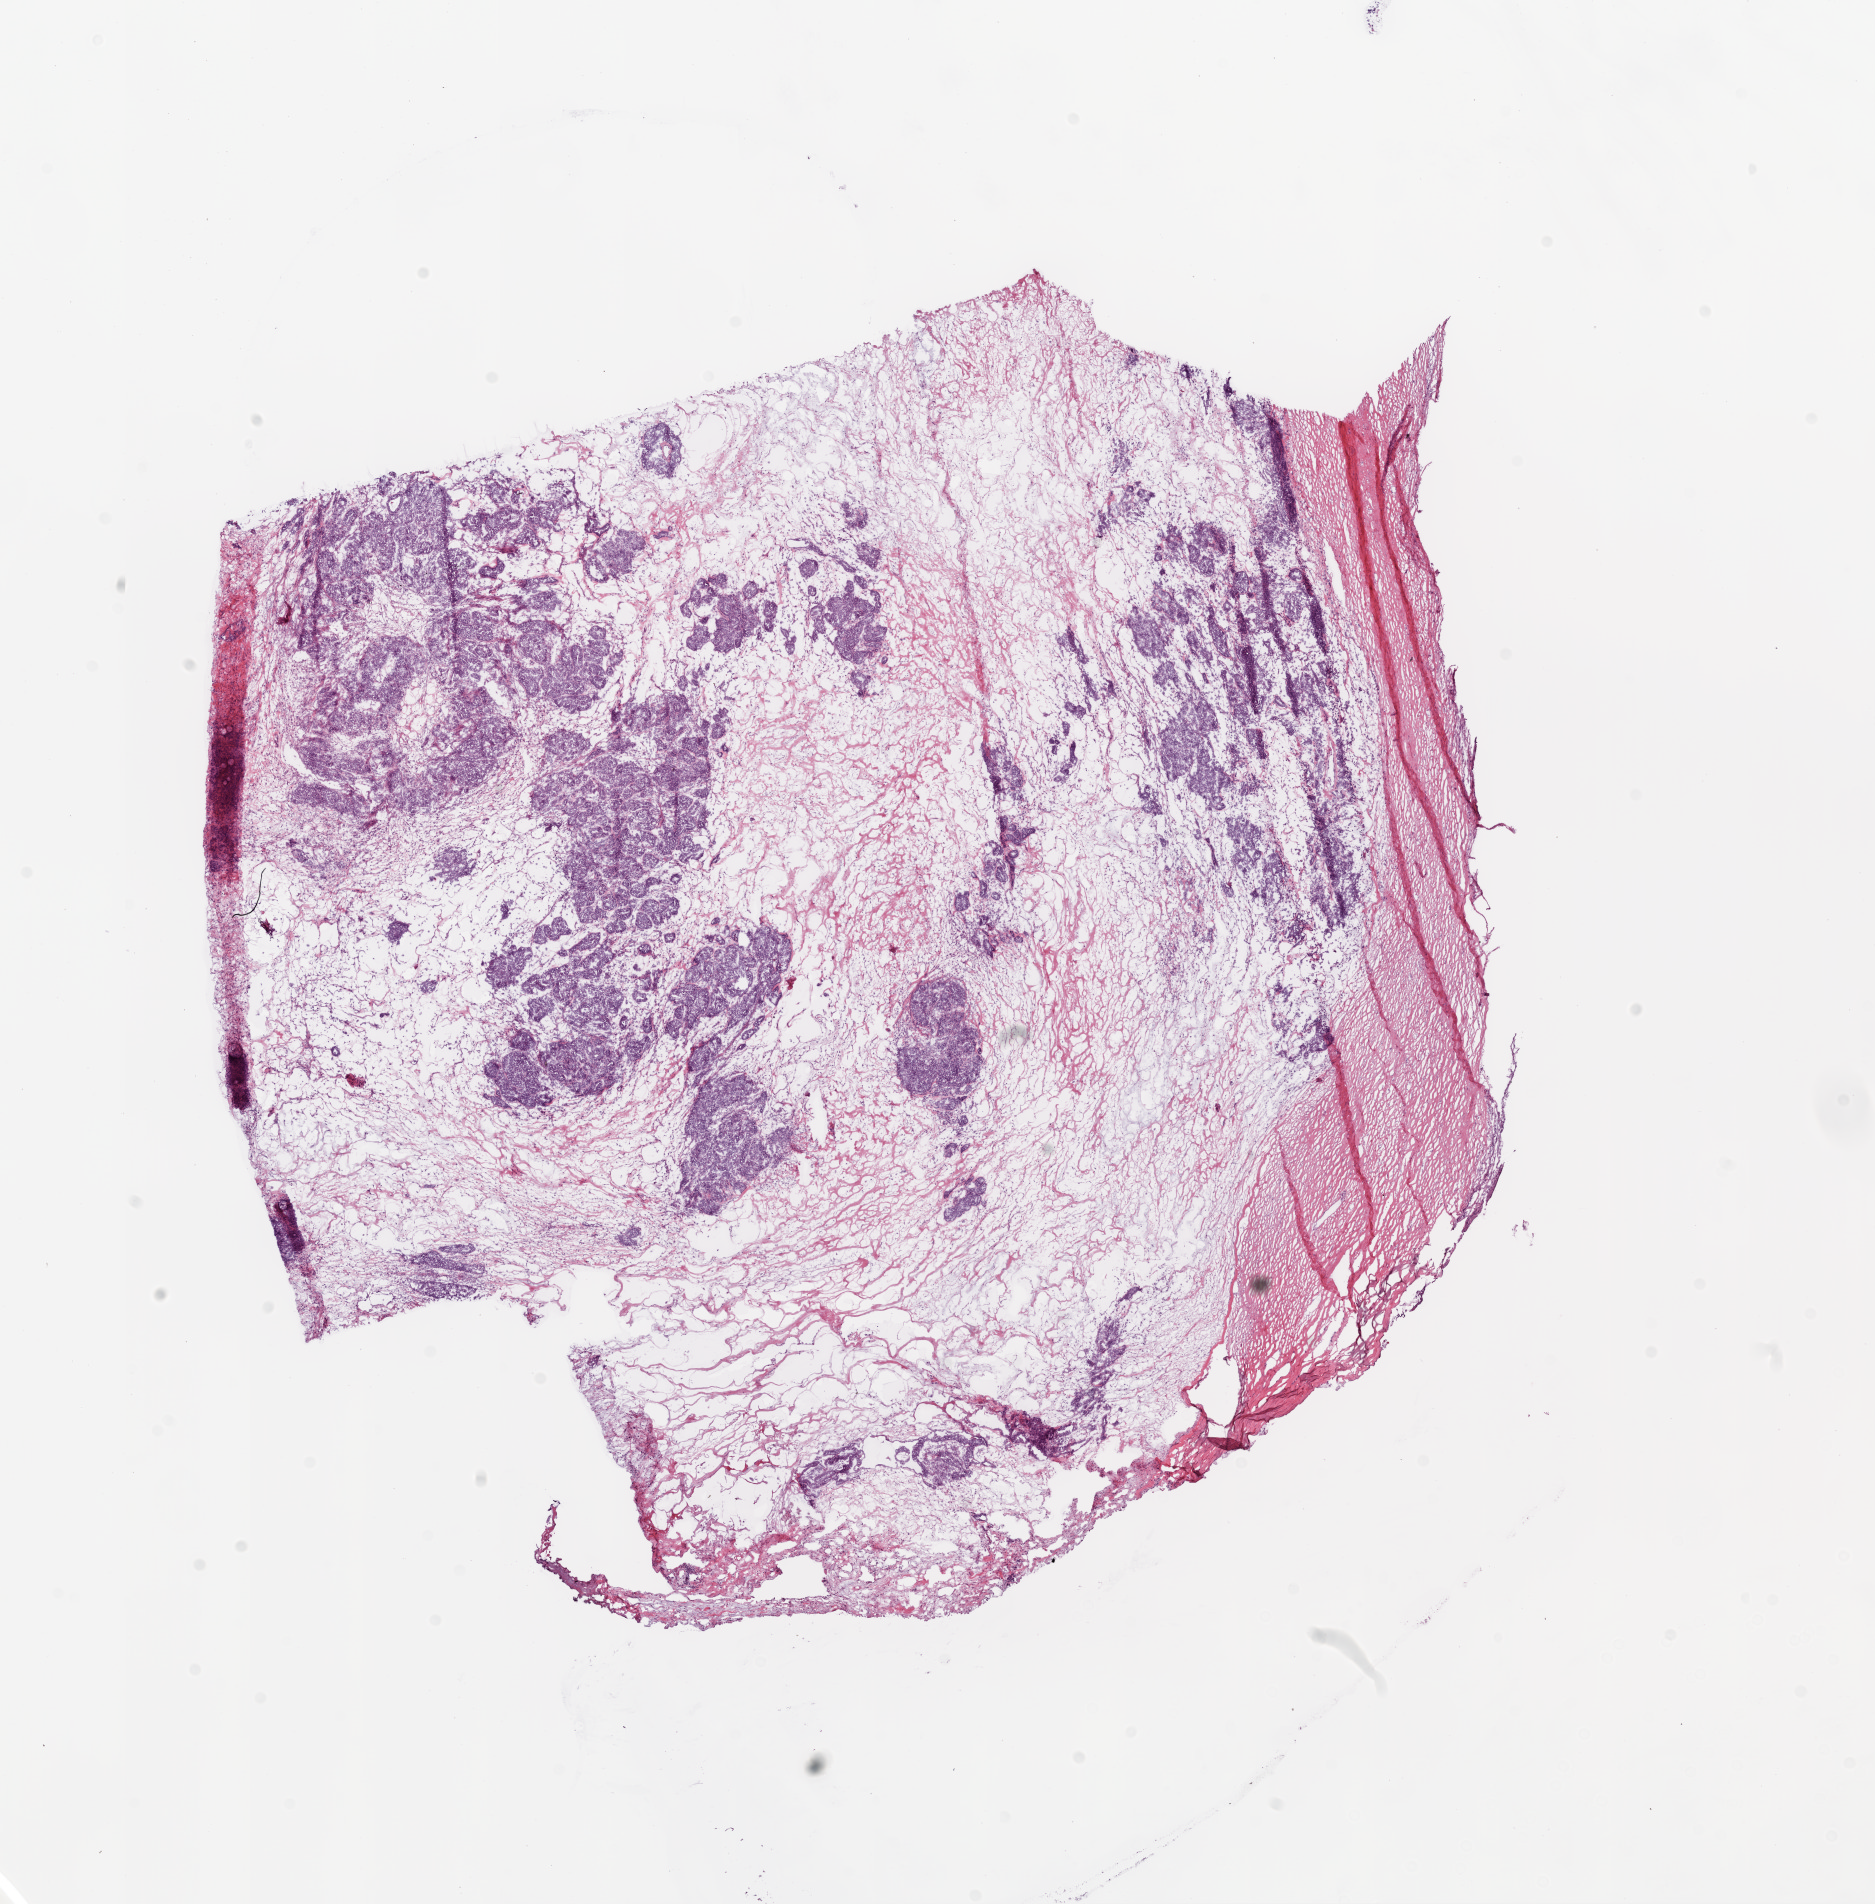
Whole-slide histology image, Hematoxylin and eosin (H&E) stained, whole scanned area (about 15.0 x 15.3 mm, acquisition: 20x scan) shown as a low-resolution overview, frozen section from the bottom of the tissue portion, sample: primary tumour, ovary. Female patient; age at initial diagnosis 51 years. Histologic grade: G3 (poorly differentiated). Pathologist review of this section (percent, as recorded): tumour cells 79%, tumour nuclei 80%, normal cells 1%, stromal cells 19%, necrosis 1%.
* laterality: bilateral
* histologic diagnosis: Serous cystadenocarcinoma, NOS
* FIGO stage: IIIC